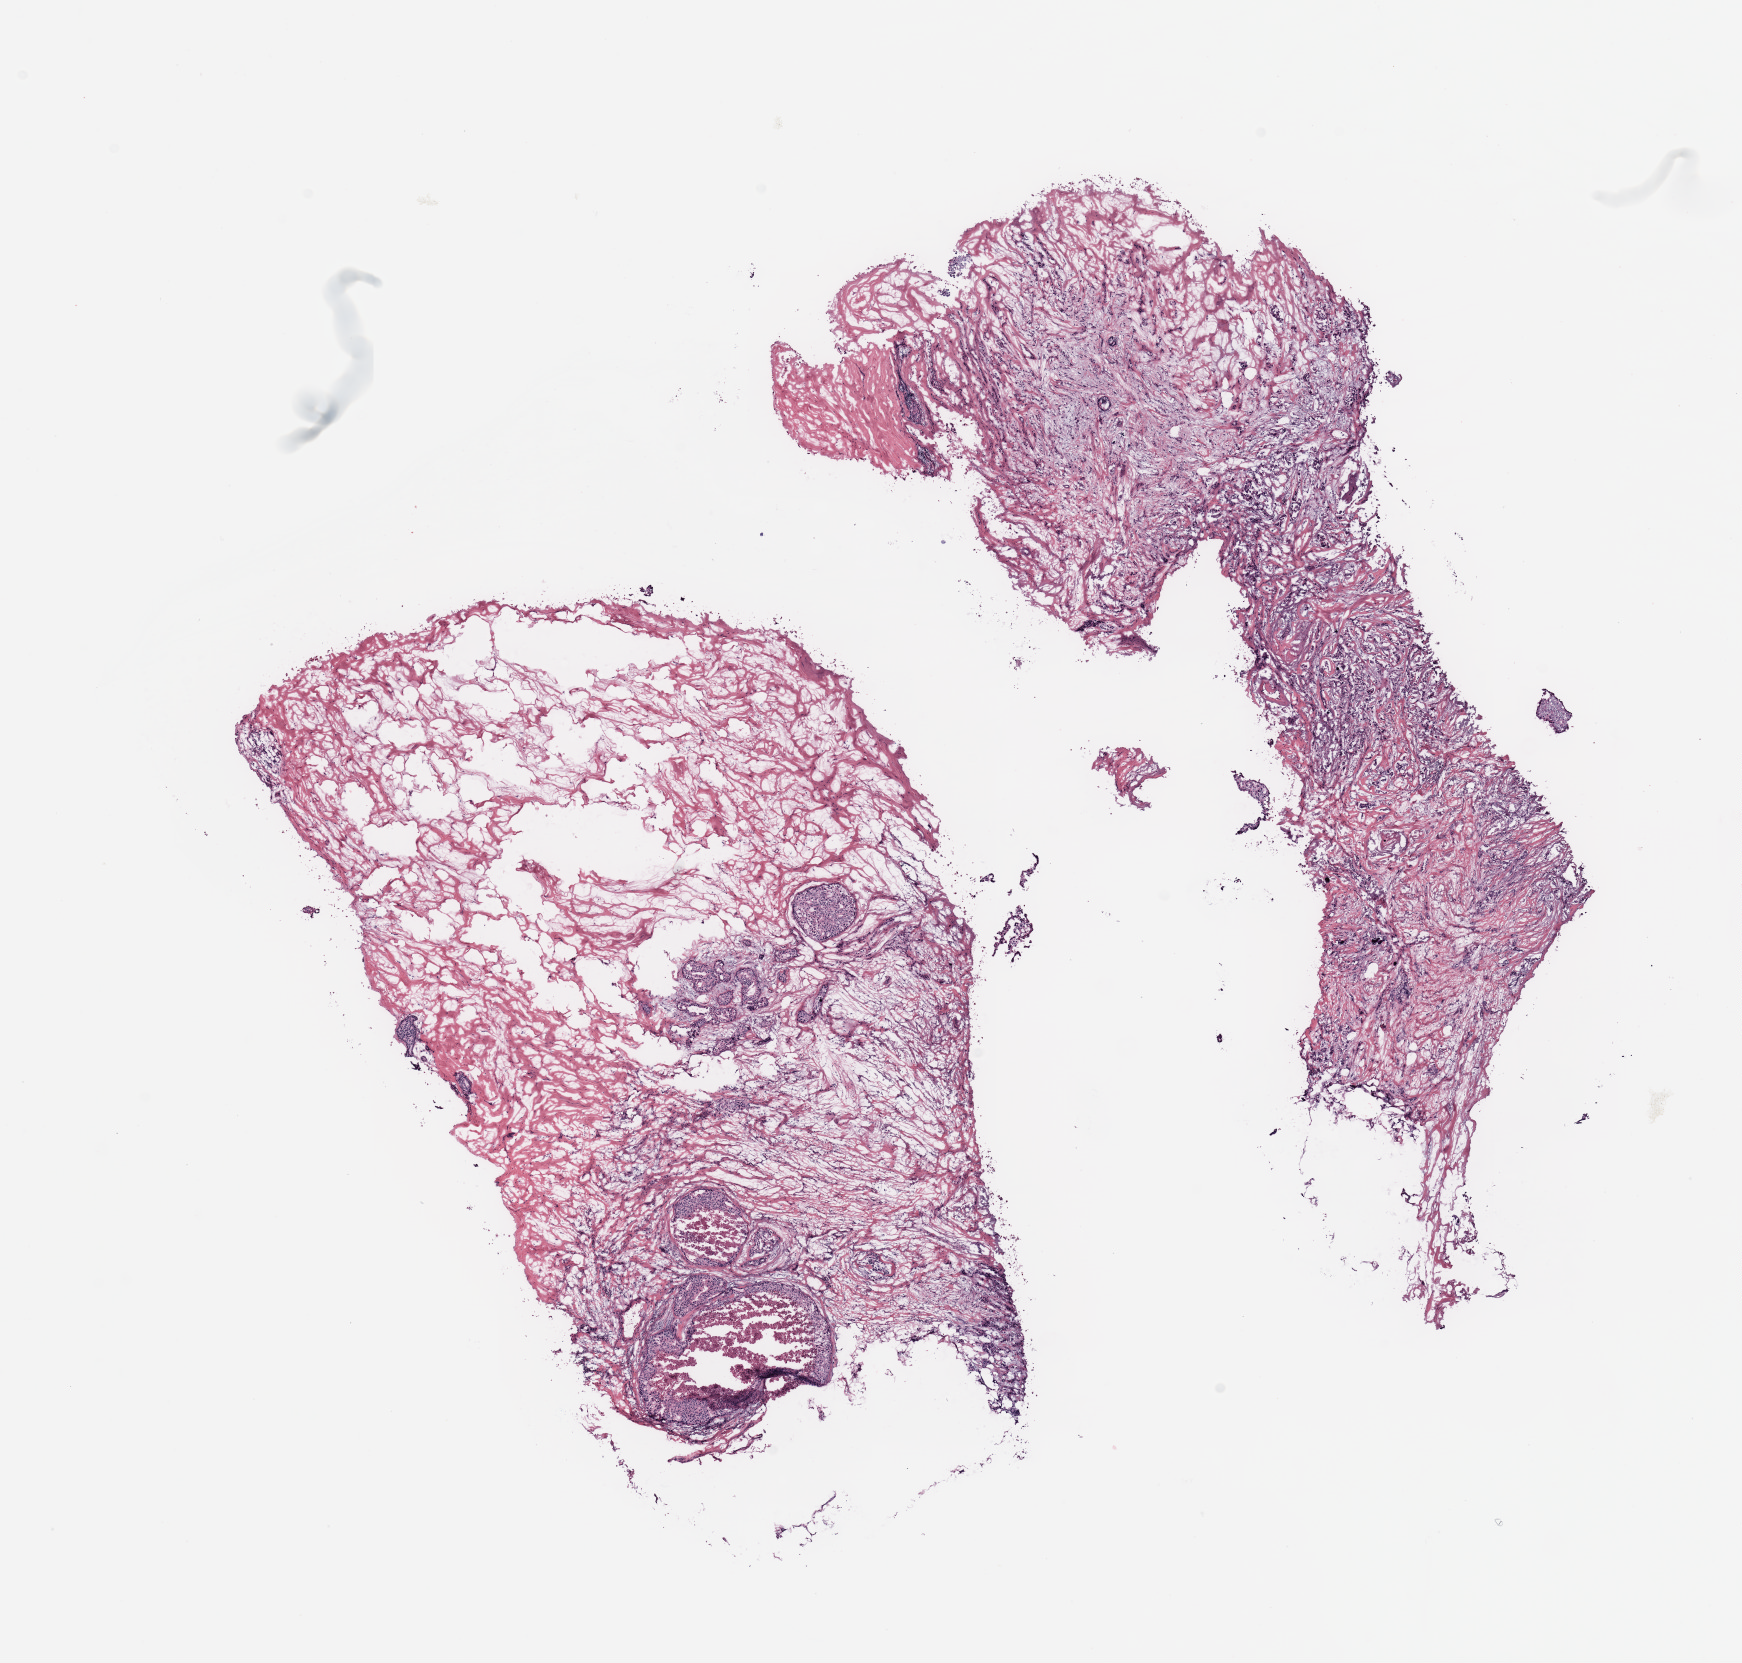
Digitized H&E-stained tissue section (whole slide), a low-resolution overview of the entire scanned area, about 13.8 x 13.2 mm (slide scanned at 20x), breast, tissue type not recorded.
Patient diagnosis (cohort enrolment): breast cancer (breast).